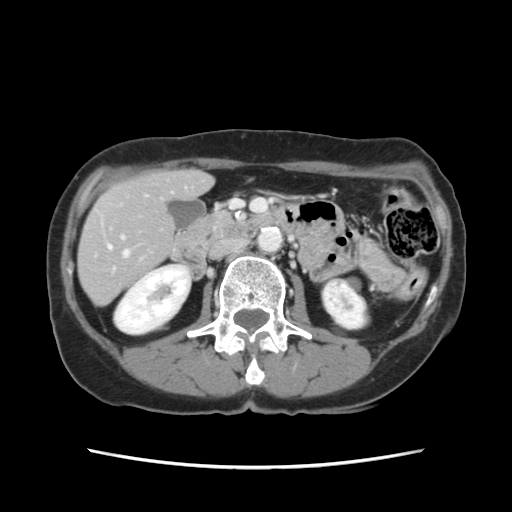
Contrast-enhanced abdominal CT, one axial slice; position 44 of 120 along the scan axis; 120 kVp; intravenous contrast given; soft-tissue window (W 400 / L 40 HU); 2.5 mm slice thickness; 512 × 512 image matrix, field of view 330 × 330 mm. Female patient, age 70 years. Case-level facts recorded for this patient, not image findings: diagnosis: colorectal cancer liver metastases, imaged before liver resection; multiple liver metastases: no; largest metastasis: 2.5 cm.
Outlined on this slice (outlined manually by an expert reader):
- hepatic veins: bounding box (x1, y1, x2, y2) in pixels: (108, 245, 129, 256)
- liver: (79, 171, 211, 303)
- planned liver remnant (the part of the liver to remain after resection): (79, 171, 211, 304)
- portal vein (with intrahepatic branches): (121, 236, 124, 239)